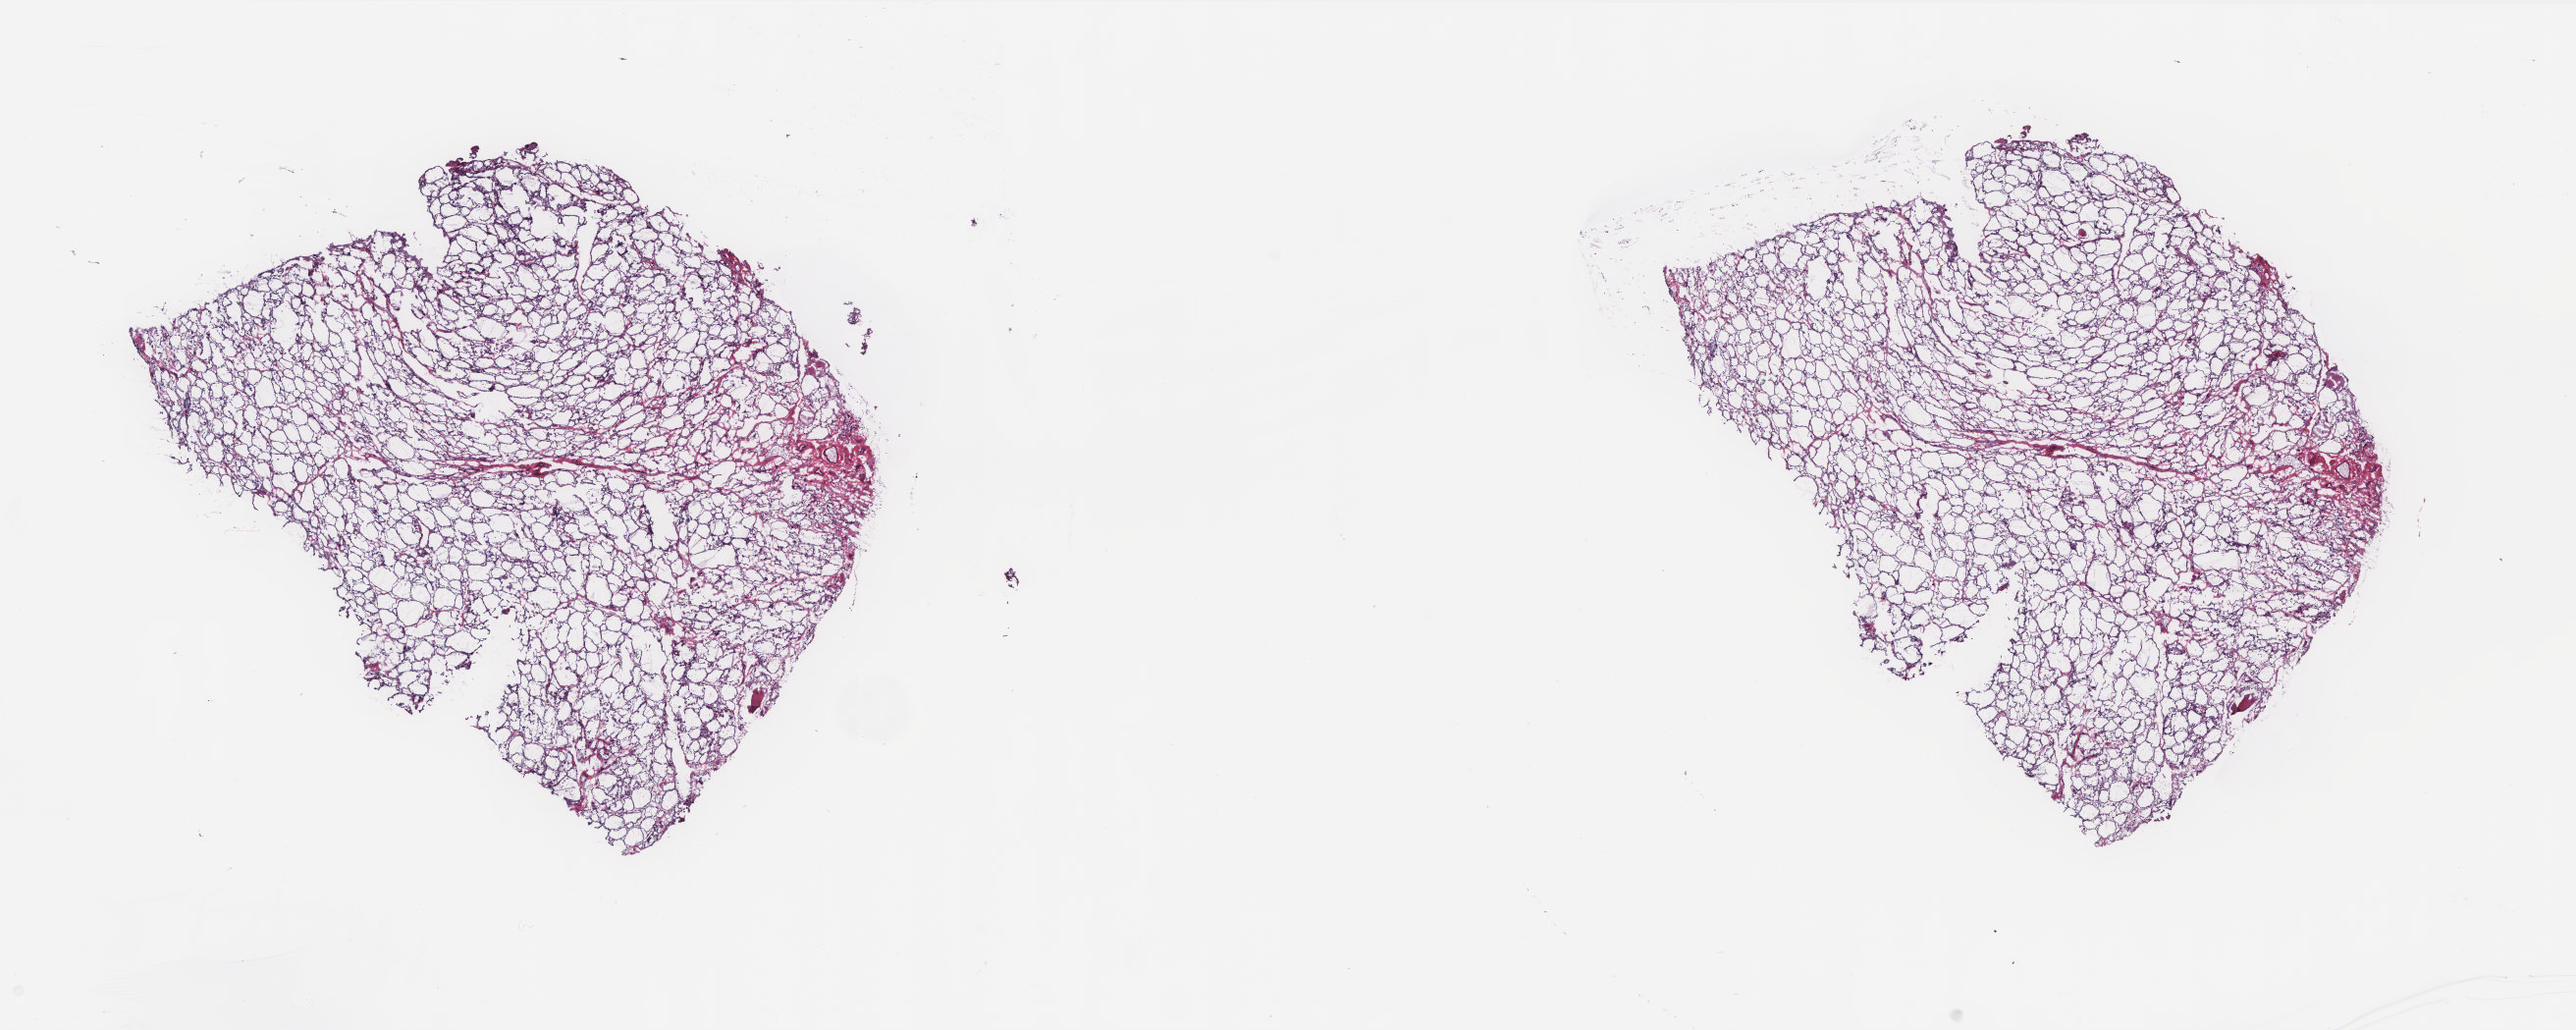
Whole-slide histology image, H&E — whole scanned area (about 21.0 x 8.4 mm) shown as a low-resolution overview; frozen section; solid tissue normal (non-tumour tissue) sample from the thyroid. Female patient; age at initial diagnosis 34 years. Slide review estimates, as recorded: tumour cells 0%, tumour nuclei 0%, normal cells 100%, stromal cells 0%, necrosis 0%. Infiltration values recorded for this section: lymphocyte infiltration 2%, monocyte infiltration 1%, neutrophil infiltration 1%.
This section: solid tissue normal (non-tumour) sample from the same patient. Patient diagnosis: Papillary adenocarcinoma, NOS.